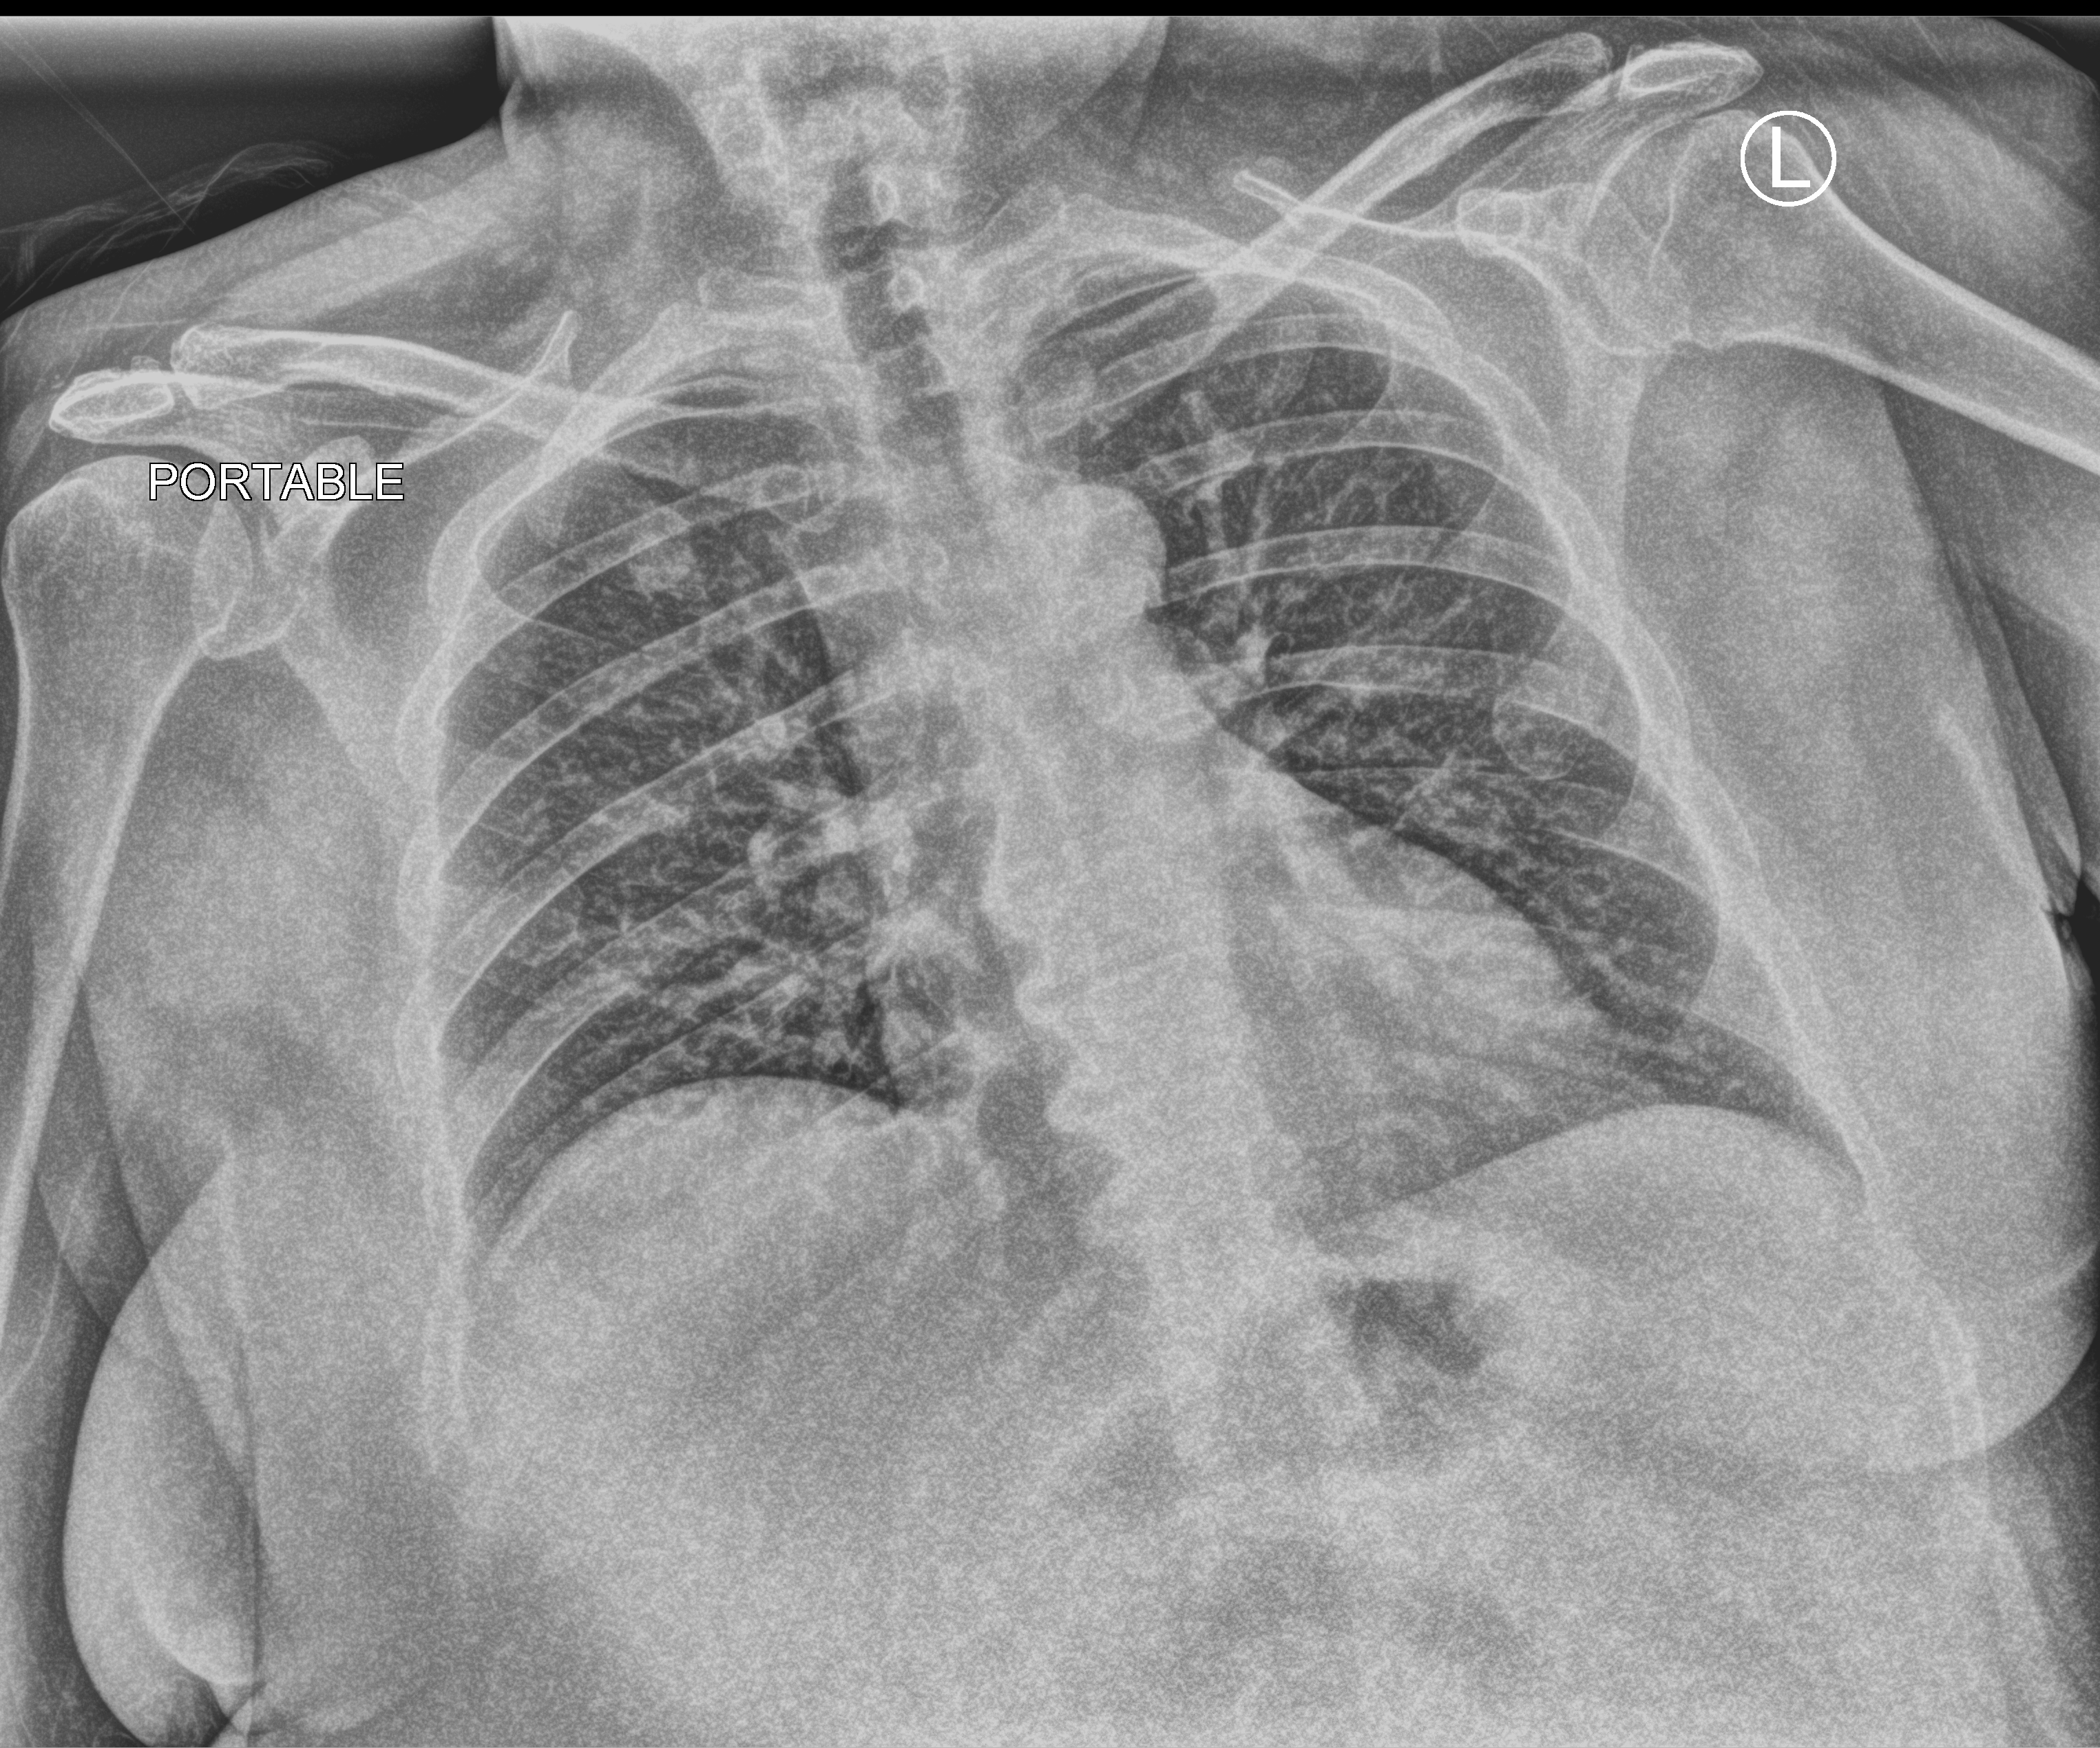
Chest X-ray (portable), anteroposterior (AP) projection. Female patient hospitalised with COVID-19, age 18–59 years.
From the hospital-stay record, not from the radiograph (when in the stay this image was taken is not recorded): mechanically ventilated during this hospital stay: no.